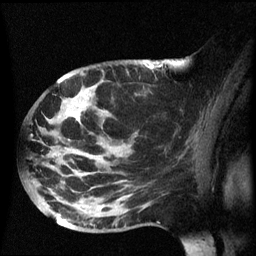
Breast MRI (dynamic contrast-enhanced), one sagittal slice. Position 38 of 60 along the scan axis. Dynamic contrast-enhanced series, image 2 of 3 at this slice position (ordered by acquisition). 1.5 T. TE 4.2 ms, TR 8.4 ms. 2.5 mm slice thickness. 256 × 256 image matrix, field of view 220 × 220 mm. Patient: female, 49 years.
Structures marked on this image (semi-automatically segmented with operator editing):
- analysis volume of interest (the breast-tissue region the enhancement analysis was run in; not a lesion): box from (x=26, y=72) to (x=158, y=233) px
- tumour enhancement mask (voxels above the 70 % enhancement threshold inside the analysis volume of interest): (x=70, y=112)–(x=80, y=121)